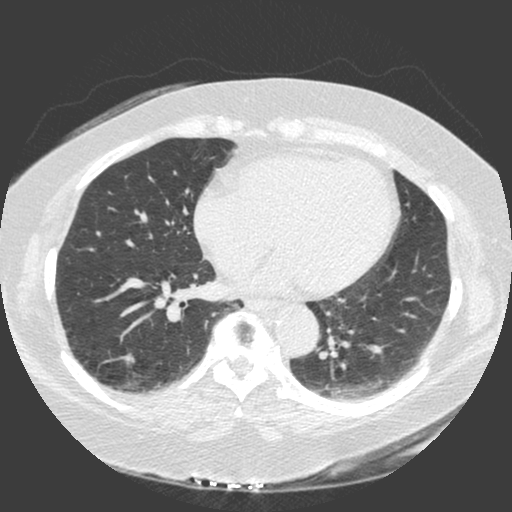
Axial slice from a low-dose chest CT screening exam, second screening round (one year after baseline), lung window (W 1500 / L -600 HU), 2 mm slice thickness, slice 101 of 175 in the series. Female, age 56 years at enrolment.
Expert reader's lesion annotation, bounding box (x1, y1, x2, y2) in pixels: (110, 343, 147, 378). No non-calcified nodule or mass ≥4 mm was recorded by the screening reader at this exam. Official screen result: negative screen, no significant abnormalities. Participant outcome: lung cancer diagnosed 440 days after this screen — adenosquamous carcinoma, right lower lobe, poorly differentiated (G3), stage IA (AJCC 6th edition), 25 mm at pathology.